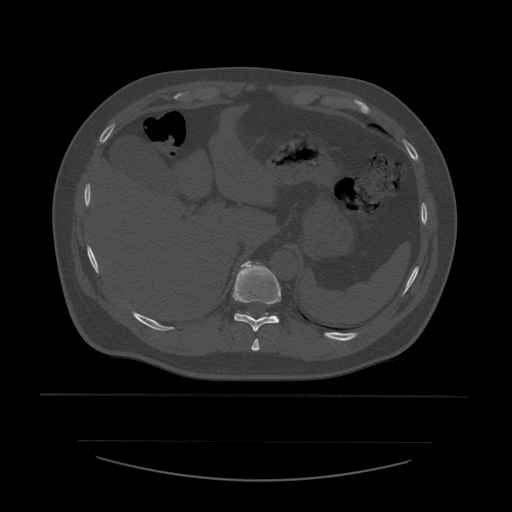
CT including the spine, one axial slice. Position 293 of 532 along the scan axis. Reconstruction kernel STANDARD. 120 kVp. Bone window (W 1800 / L 400 HU). 1.25 mm slice thickness. 512 × 512 image matrix, field of view 441 × 441 mm. Patient age 44 years. Case-level facts recorded for this patient, not image findings: primary cancer: soft tissue sarcoma.
Outlined on this slice (semi-automatically segmented with operator editing):
- T10 vertebra: box from (x=233, y=261) to (x=282, y=332) px
- T9 vertebra: (x=251, y=339)–(x=260, y=352)